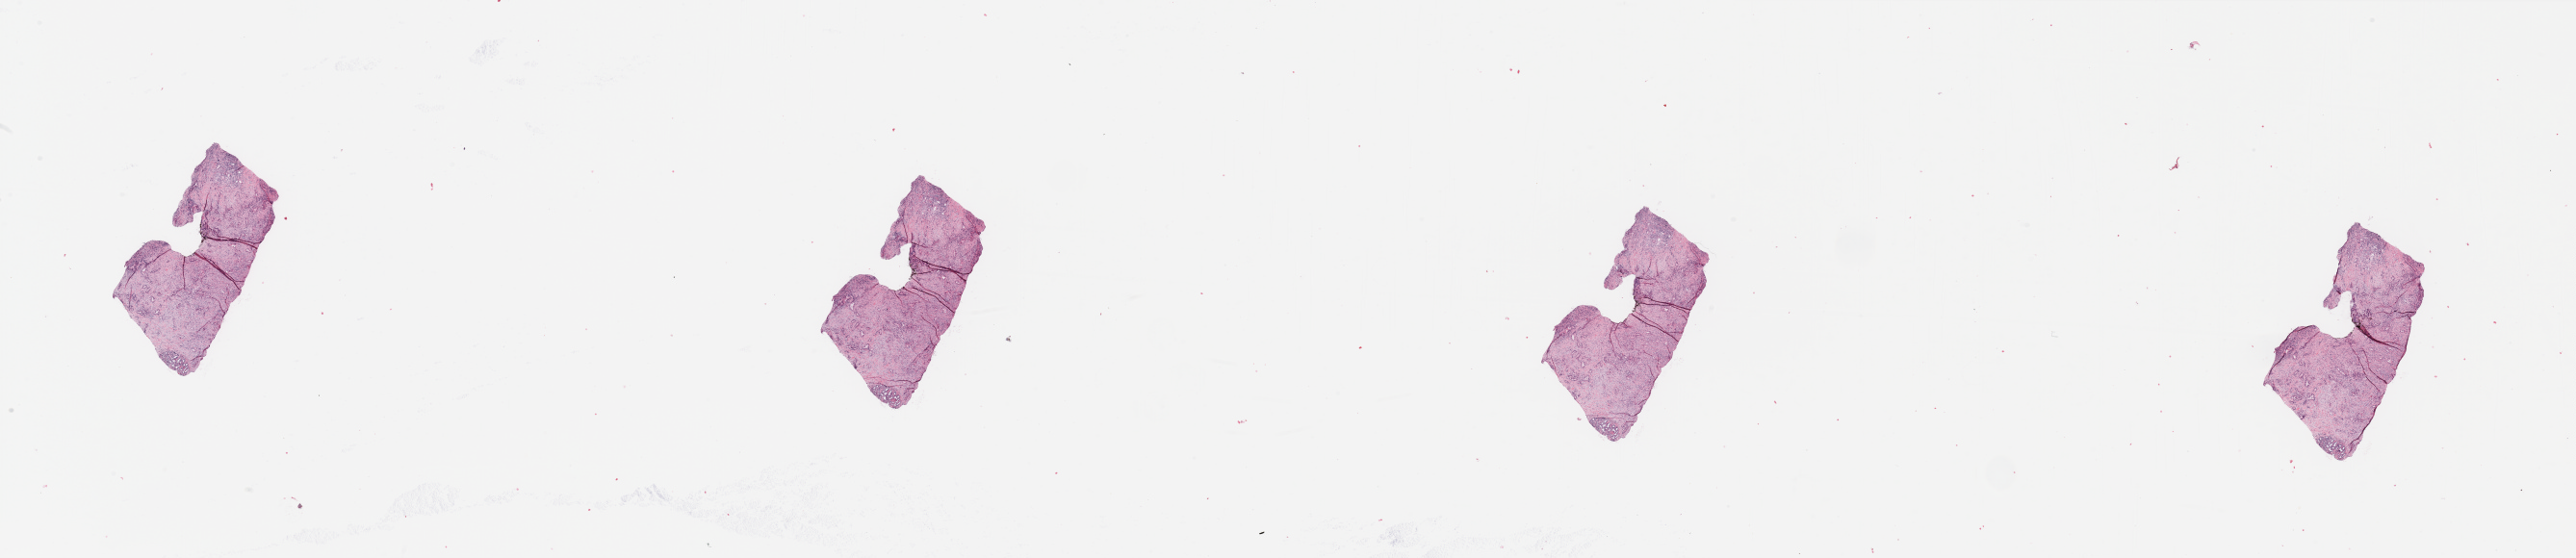
Digitized Hematoxylin and eosin (H&E) stained tissue section (whole slide) — low-resolution overview of the scanned area, about 42.3 x 9.2 mm (slide scanned at 20x); tumour tissue sample, sampled site: pancreas. Male, 78 y/o. Histologic grade: G2 (moderately differentiated). Composition of this section per pathologist review: tumour nuclei 30%, necrosis 0%.
Histologic diagnosis: Infiltrating duct carcinoma, NOS. Primary tumour site (as recorded): head. AJCC pathologic stage: IIB.